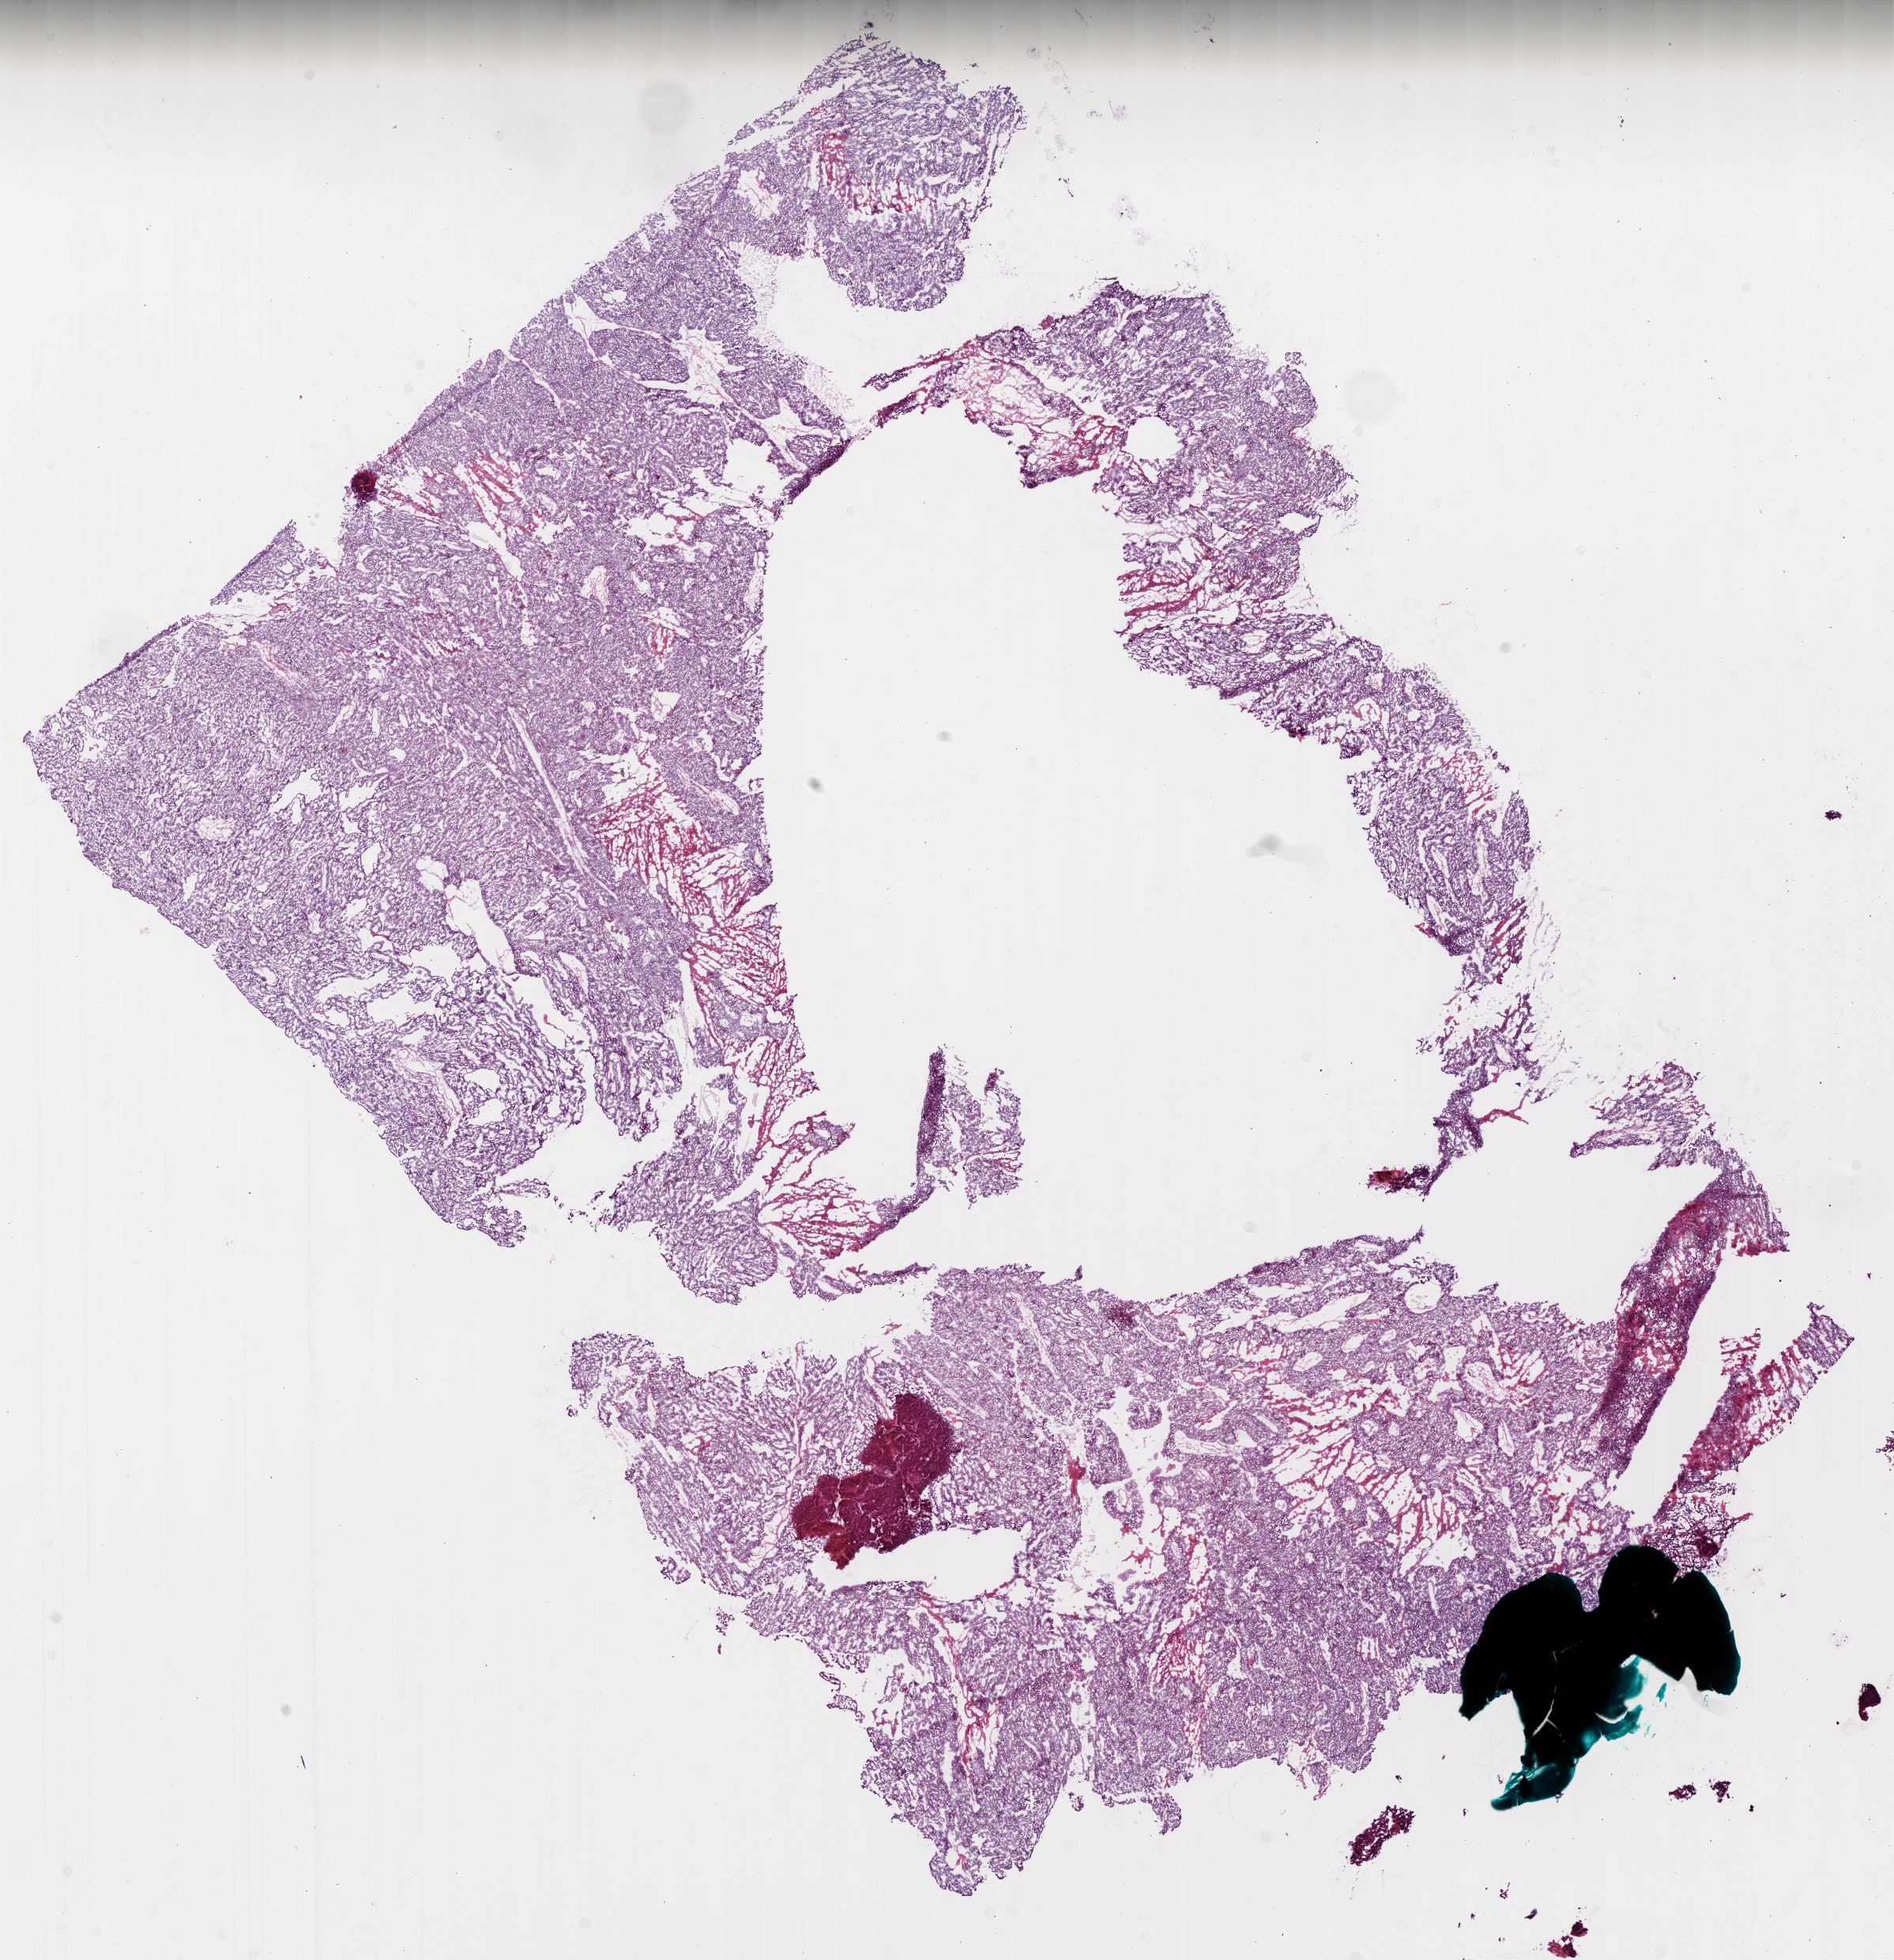
H&E whole-slide image — whole scanned area (about 19.3 x 19.9 mm) shown as a low-resolution overview; frozen section from the bottom of the tissue portion; primary tumour sample from the ovary. Female patient; age at initial diagnosis 44 years. Histologic grade: G3 (poorly differentiated). Composition of this section per pathologist review: tumour cells 90%, tumour nuclei 98%, normal cells 0%, stromal cells 10%, necrosis 0%.
- pathologic diagnosis: Serous cystadenocarcinoma, NOS
- FIGO stage: IIIC
- laterality: bilateral